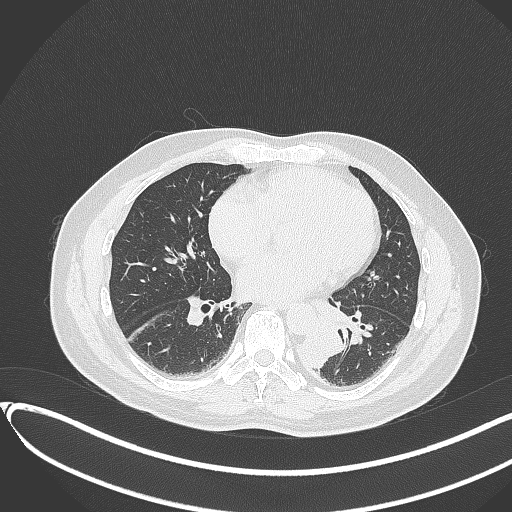
Chest CT, one axial slice; position 139 of 417 along the scan axis; reconstruction kernel B70f; 120 kVp; lung window (W 1500 / L -600 HU); 512 × 512 image matrix. Male patient, age 54 years. Case-level facts recorded for this patient, not image findings: clinical TNM (as recorded): T3 N0 M0.
Annotated regions visible in this slice (rectangle marked by the reading radiologist):
- lung tumour (recorded histology: squamous cell carcinoma): bounding box (x1, y1, x2, y2) in pixels: (291, 325, 348, 372)